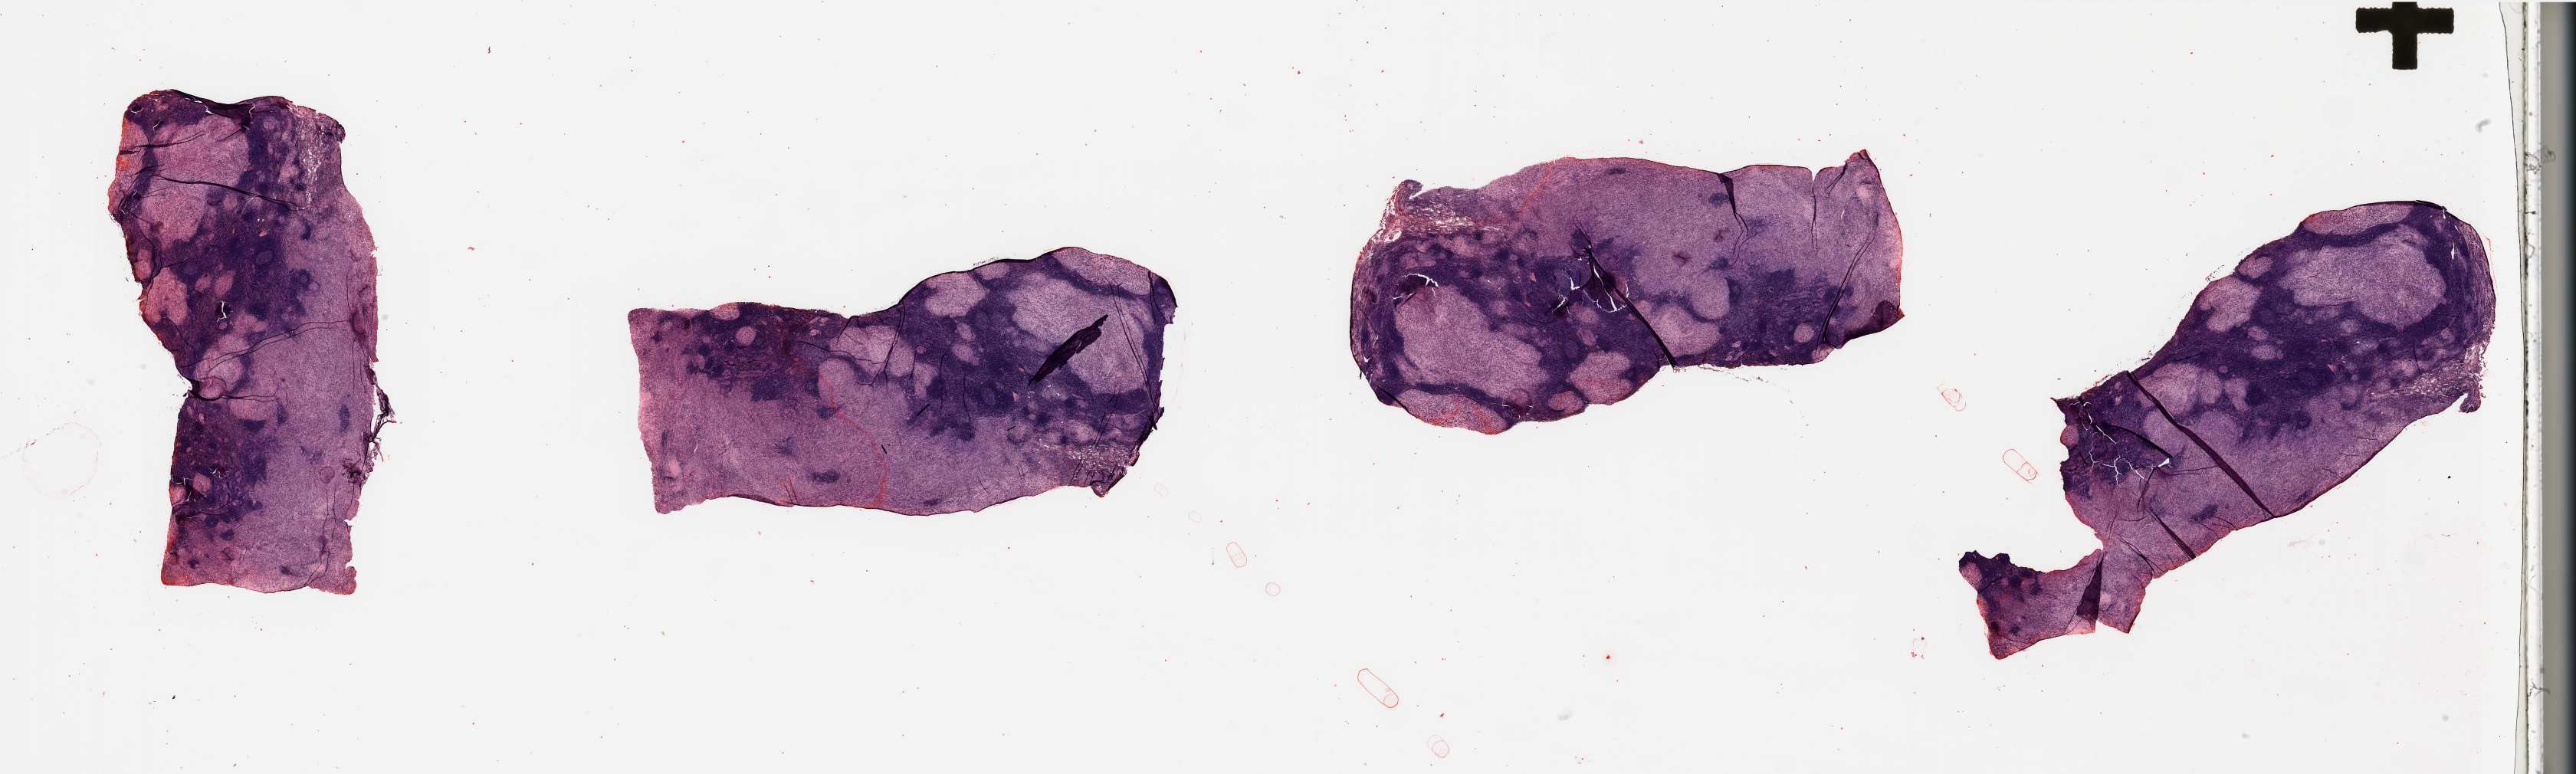
Whole-slide histology image, H&E — a low-resolution overview of the entire scanned area, about 53.2 x 16.0 mm. Tumour tissue sample, sampled site: lymph node. Patient: female, age 58 years.
Patient diagnosis: Malignant melanoma, NOS.